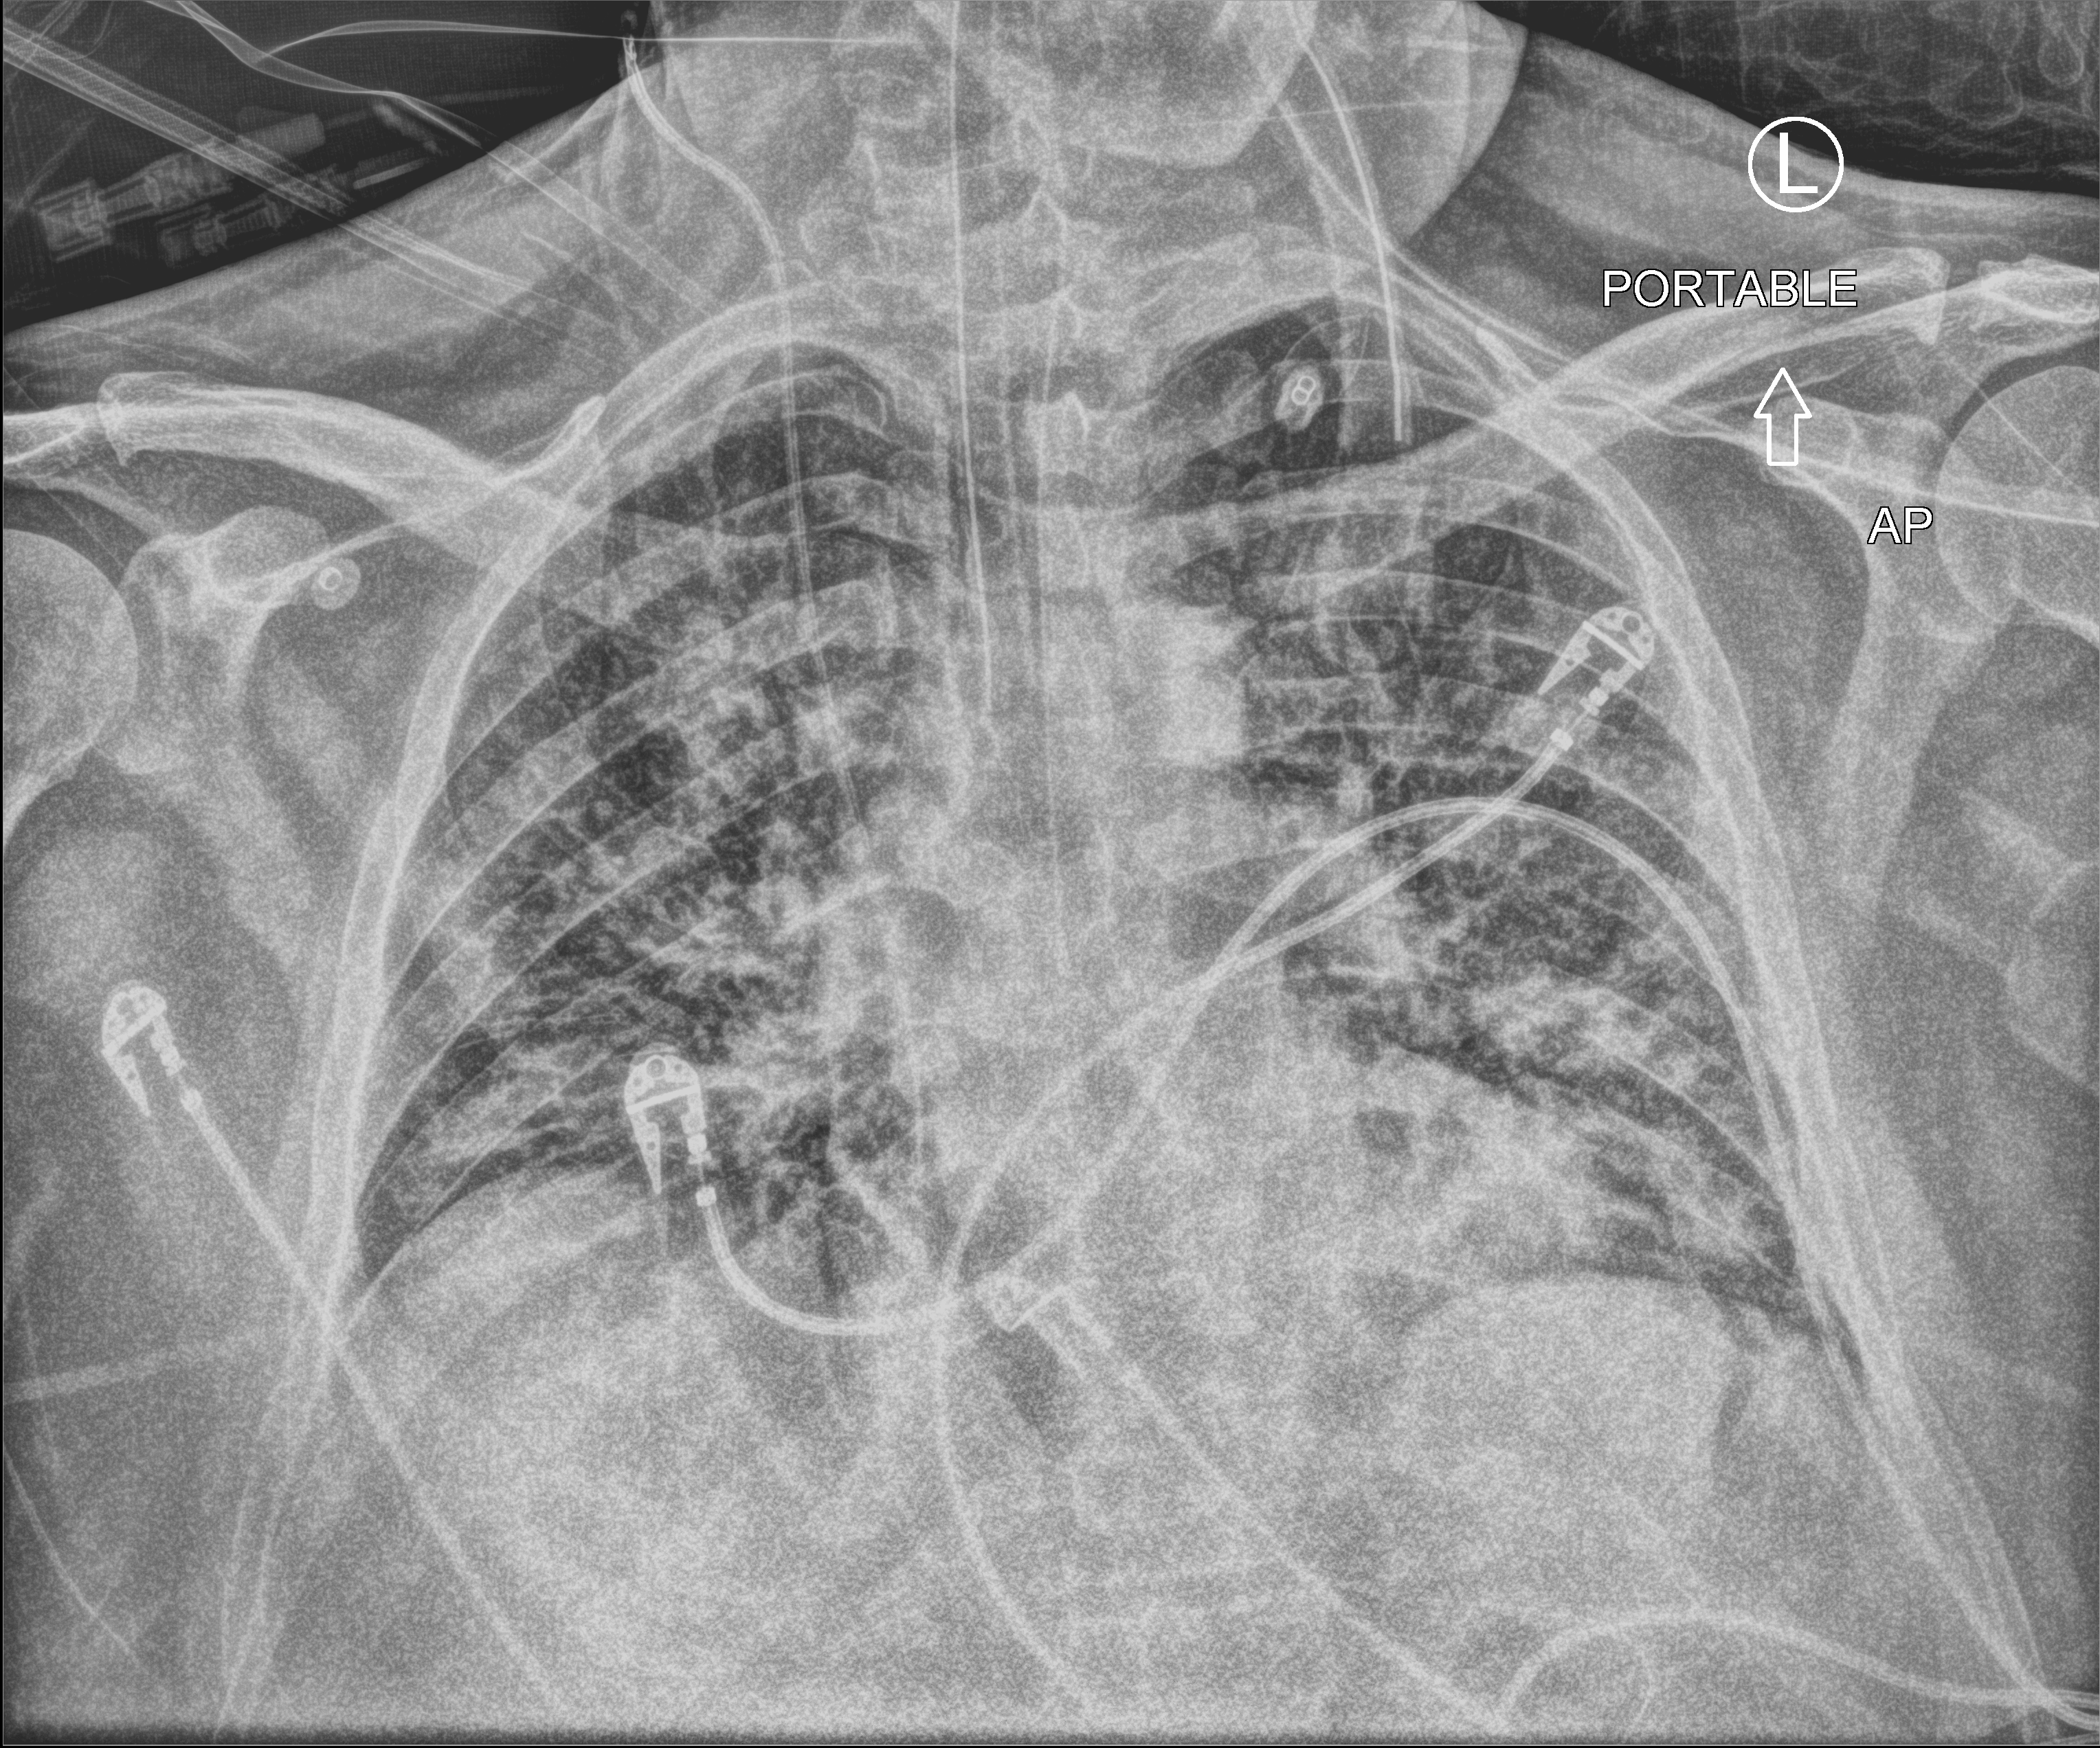
Portable chest radiograph, anteroposterior (AP) projection. Male patient hospitalised with COVID-19, age 18–59 years.
Admission-level facts for this patient (not findings on this image; timing relative to this image not recorded): COPD (admission record): no; diabetes (admission record): yes; admitted to intensive care during this hospital stay: yes.